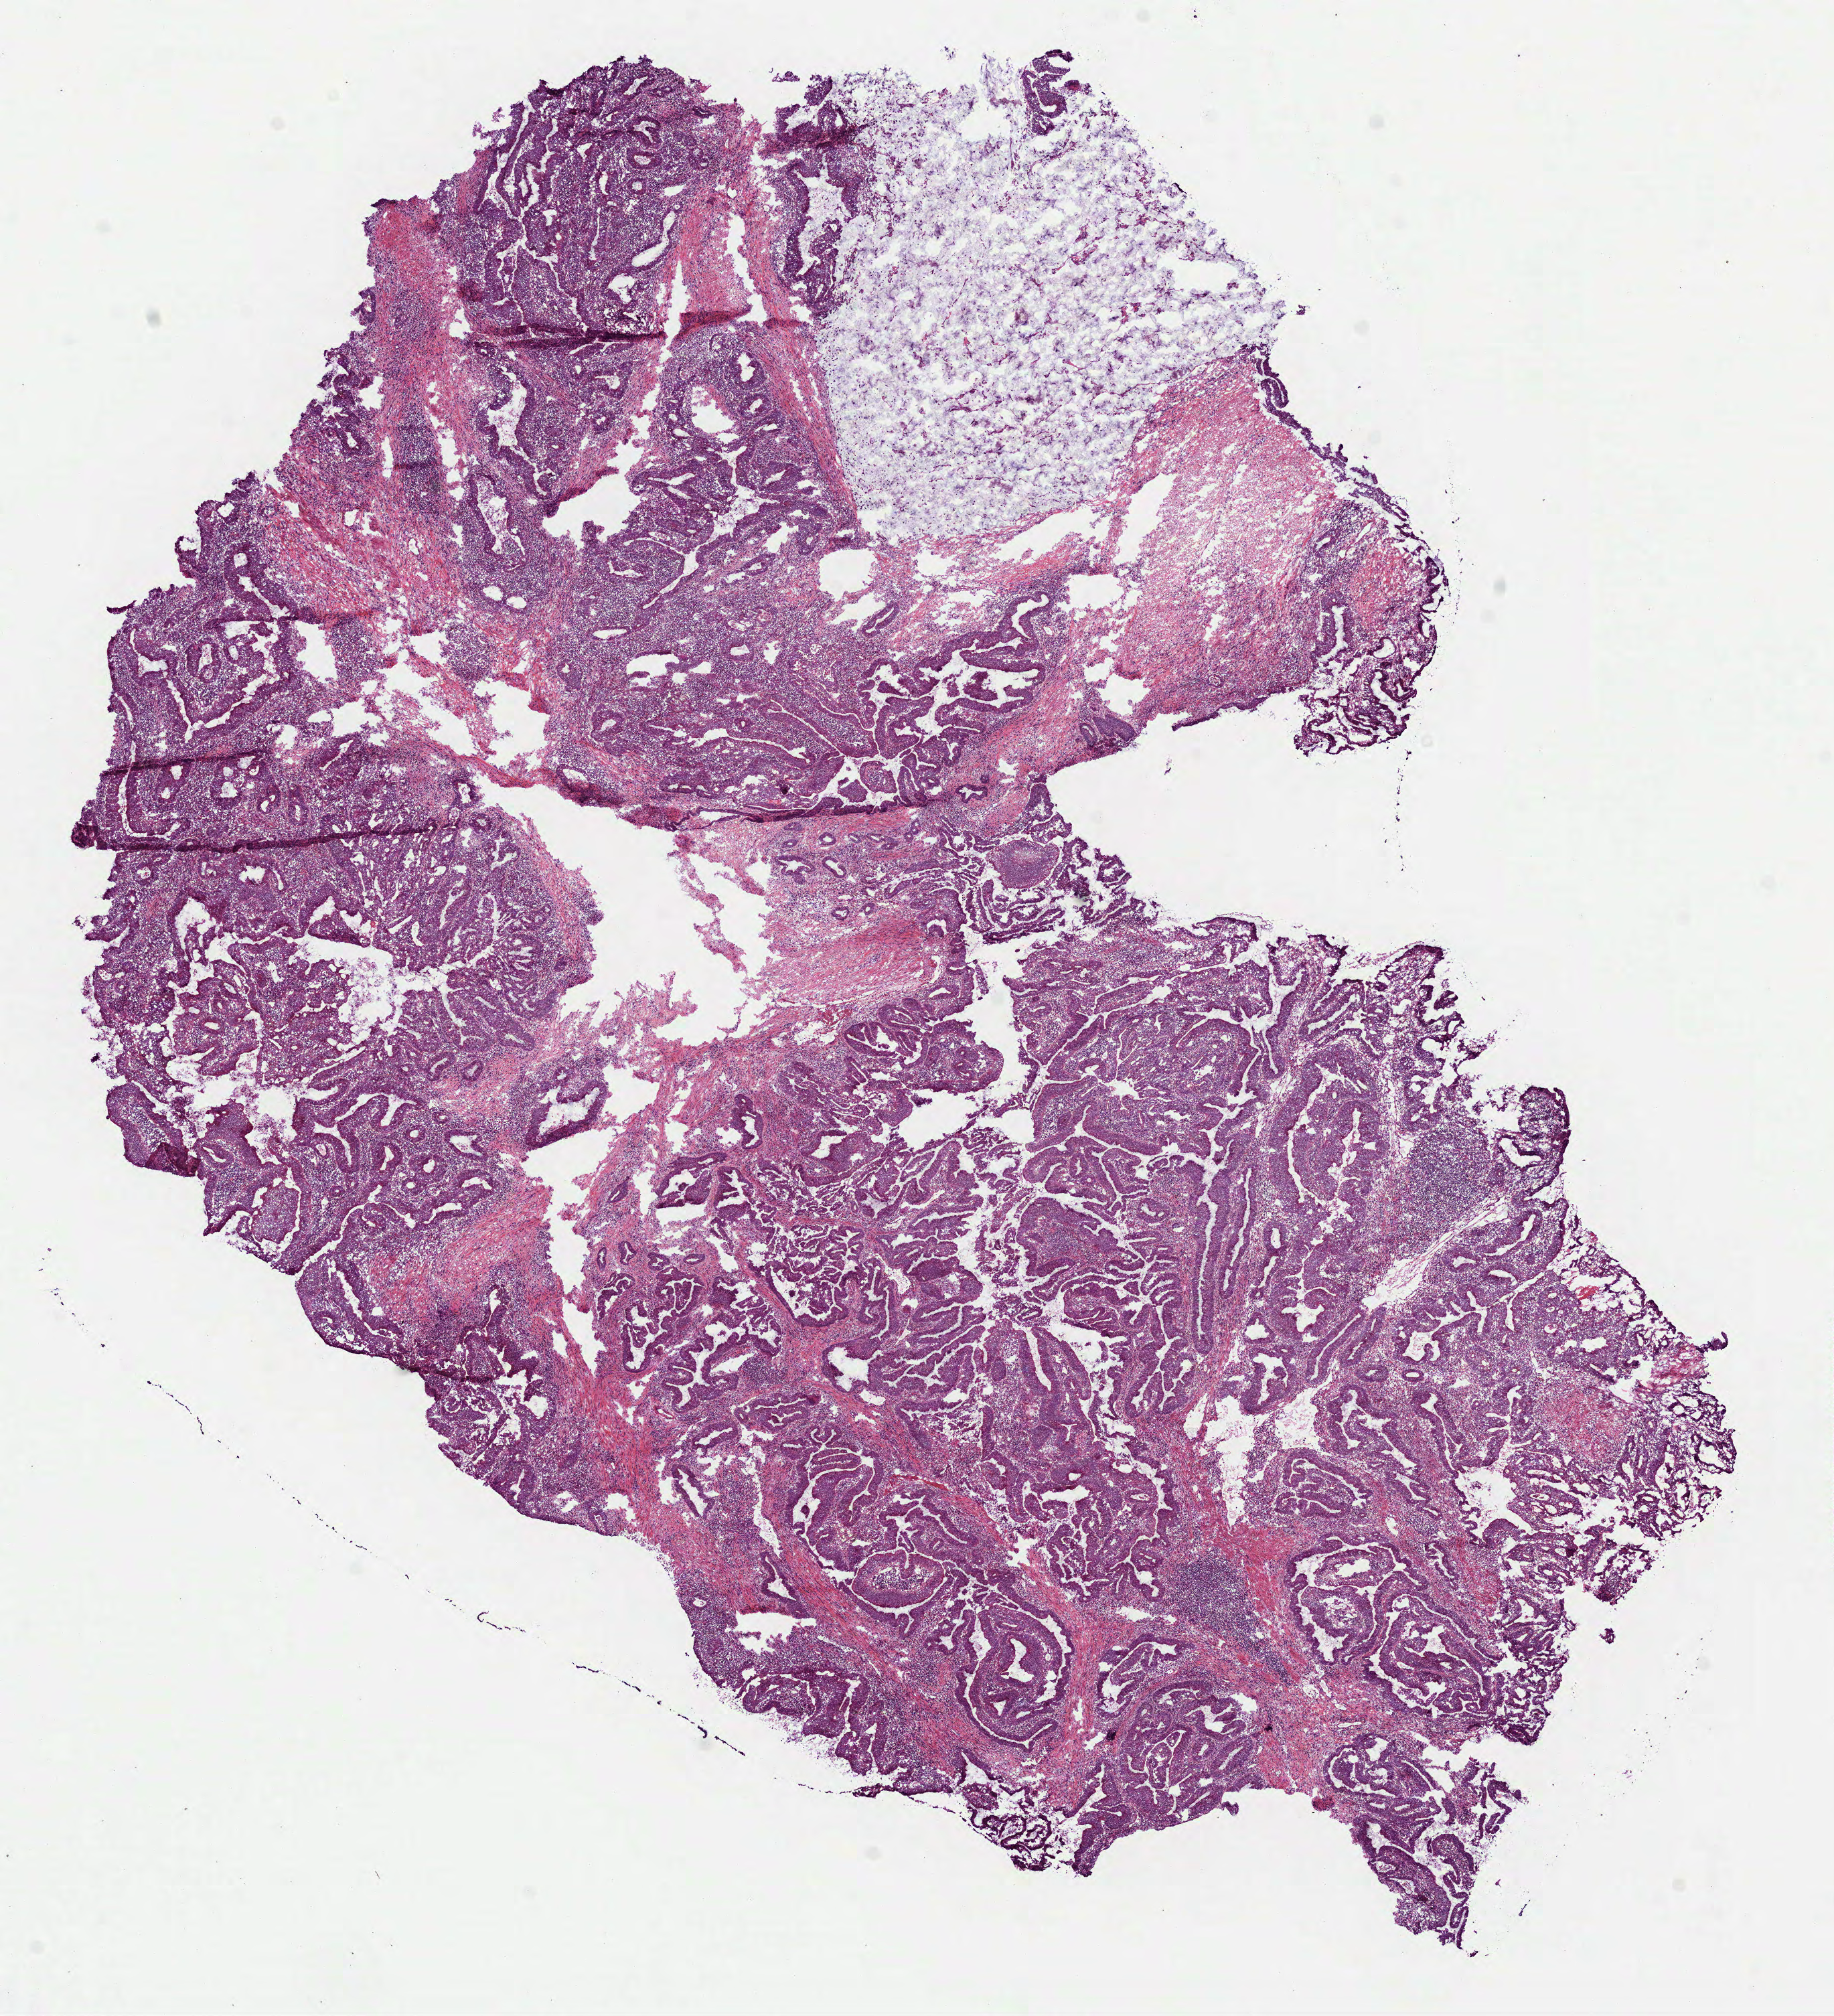
H&E-stained whole-slide image, whole scanned area (about 11.0 x 12.1 mm, from a 40x scan) shown as a low-resolution overview. Frozen section. Colon, primary tumour sample. Male patient; age at initial diagnosis 31 years. Composition of this section per pathologist review: tumour cells 99%, tumour nuclei 50%.
Diagnosis: Adenocarcinoma, NOS.